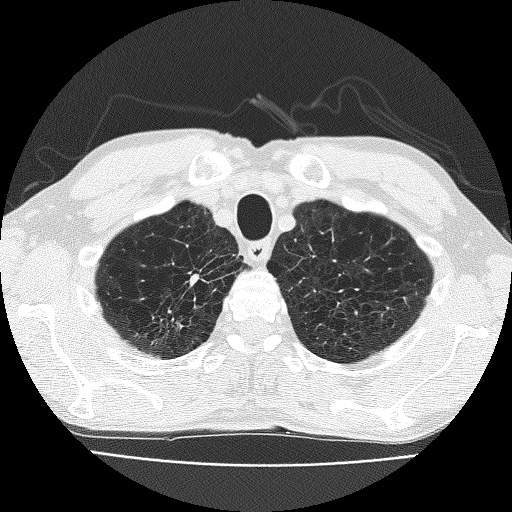
Low-dose screening chest CT, one axial slice. Slice 152 of 185 in the series (ordered by position). Reconstruction kernel FC51. 120 kVp. Lung window (W 1500 / L -600 HU). 2 mm slice thickness. 512 × 512 image matrix, field of view 322 × 322 mm.
Structures marked on this image (expert manual segmentation):
- lesion 1 (nodule, upper lobe of right lung): bounding box [x1, y1, x2, y2] px = [191, 274, 199, 285]